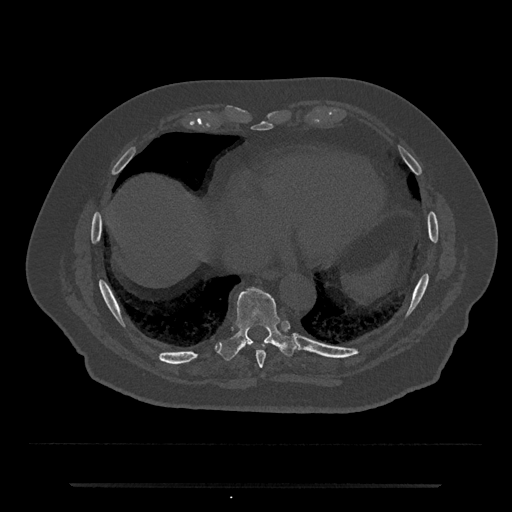
CT including the spine, one axial slice. Position 772 of 797 along the scan axis. 120 kVp. Bone window (W 1800 / L 400 HU). 0.5 mm slice thickness. 512 × 512 image matrix. Male patient, age 80 years. Case-level facts recorded for this patient, not image findings: primary cancer: prostate; vertebrae with lytic lesions (as recorded): L1, T11.
Structures marked on this image (semi-automatically segmented with operator editing):
- T8 vertebra: bounding box <256,351,265,368> (left, top, right, bottom; pixels)
- T9 vertebra: <217,286,301,361>